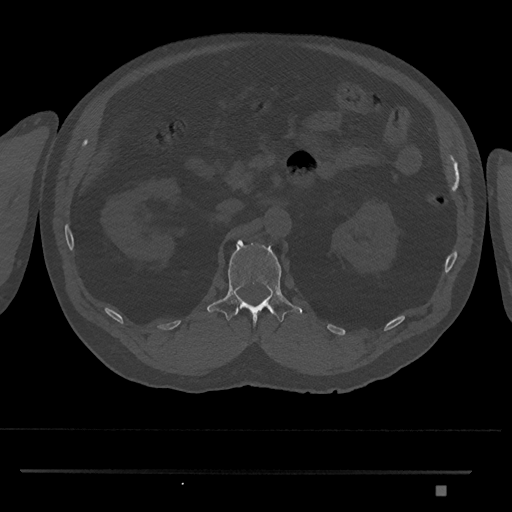
CT including the spine, one axial slice. 120 kVp. Bone window (W 1800 / L 400 HU). 512 × 512 image matrix. Patient: male, 65 years. Case-level facts recorded for this patient, not image findings: primary cancer: prostate.
Structures marked on this image (semi-automatic segmentation, software-assisted and operator-edited):
- L1 vertebra: bounding box [x1, y1, x2, y2] px = [207, 239, 303, 327]